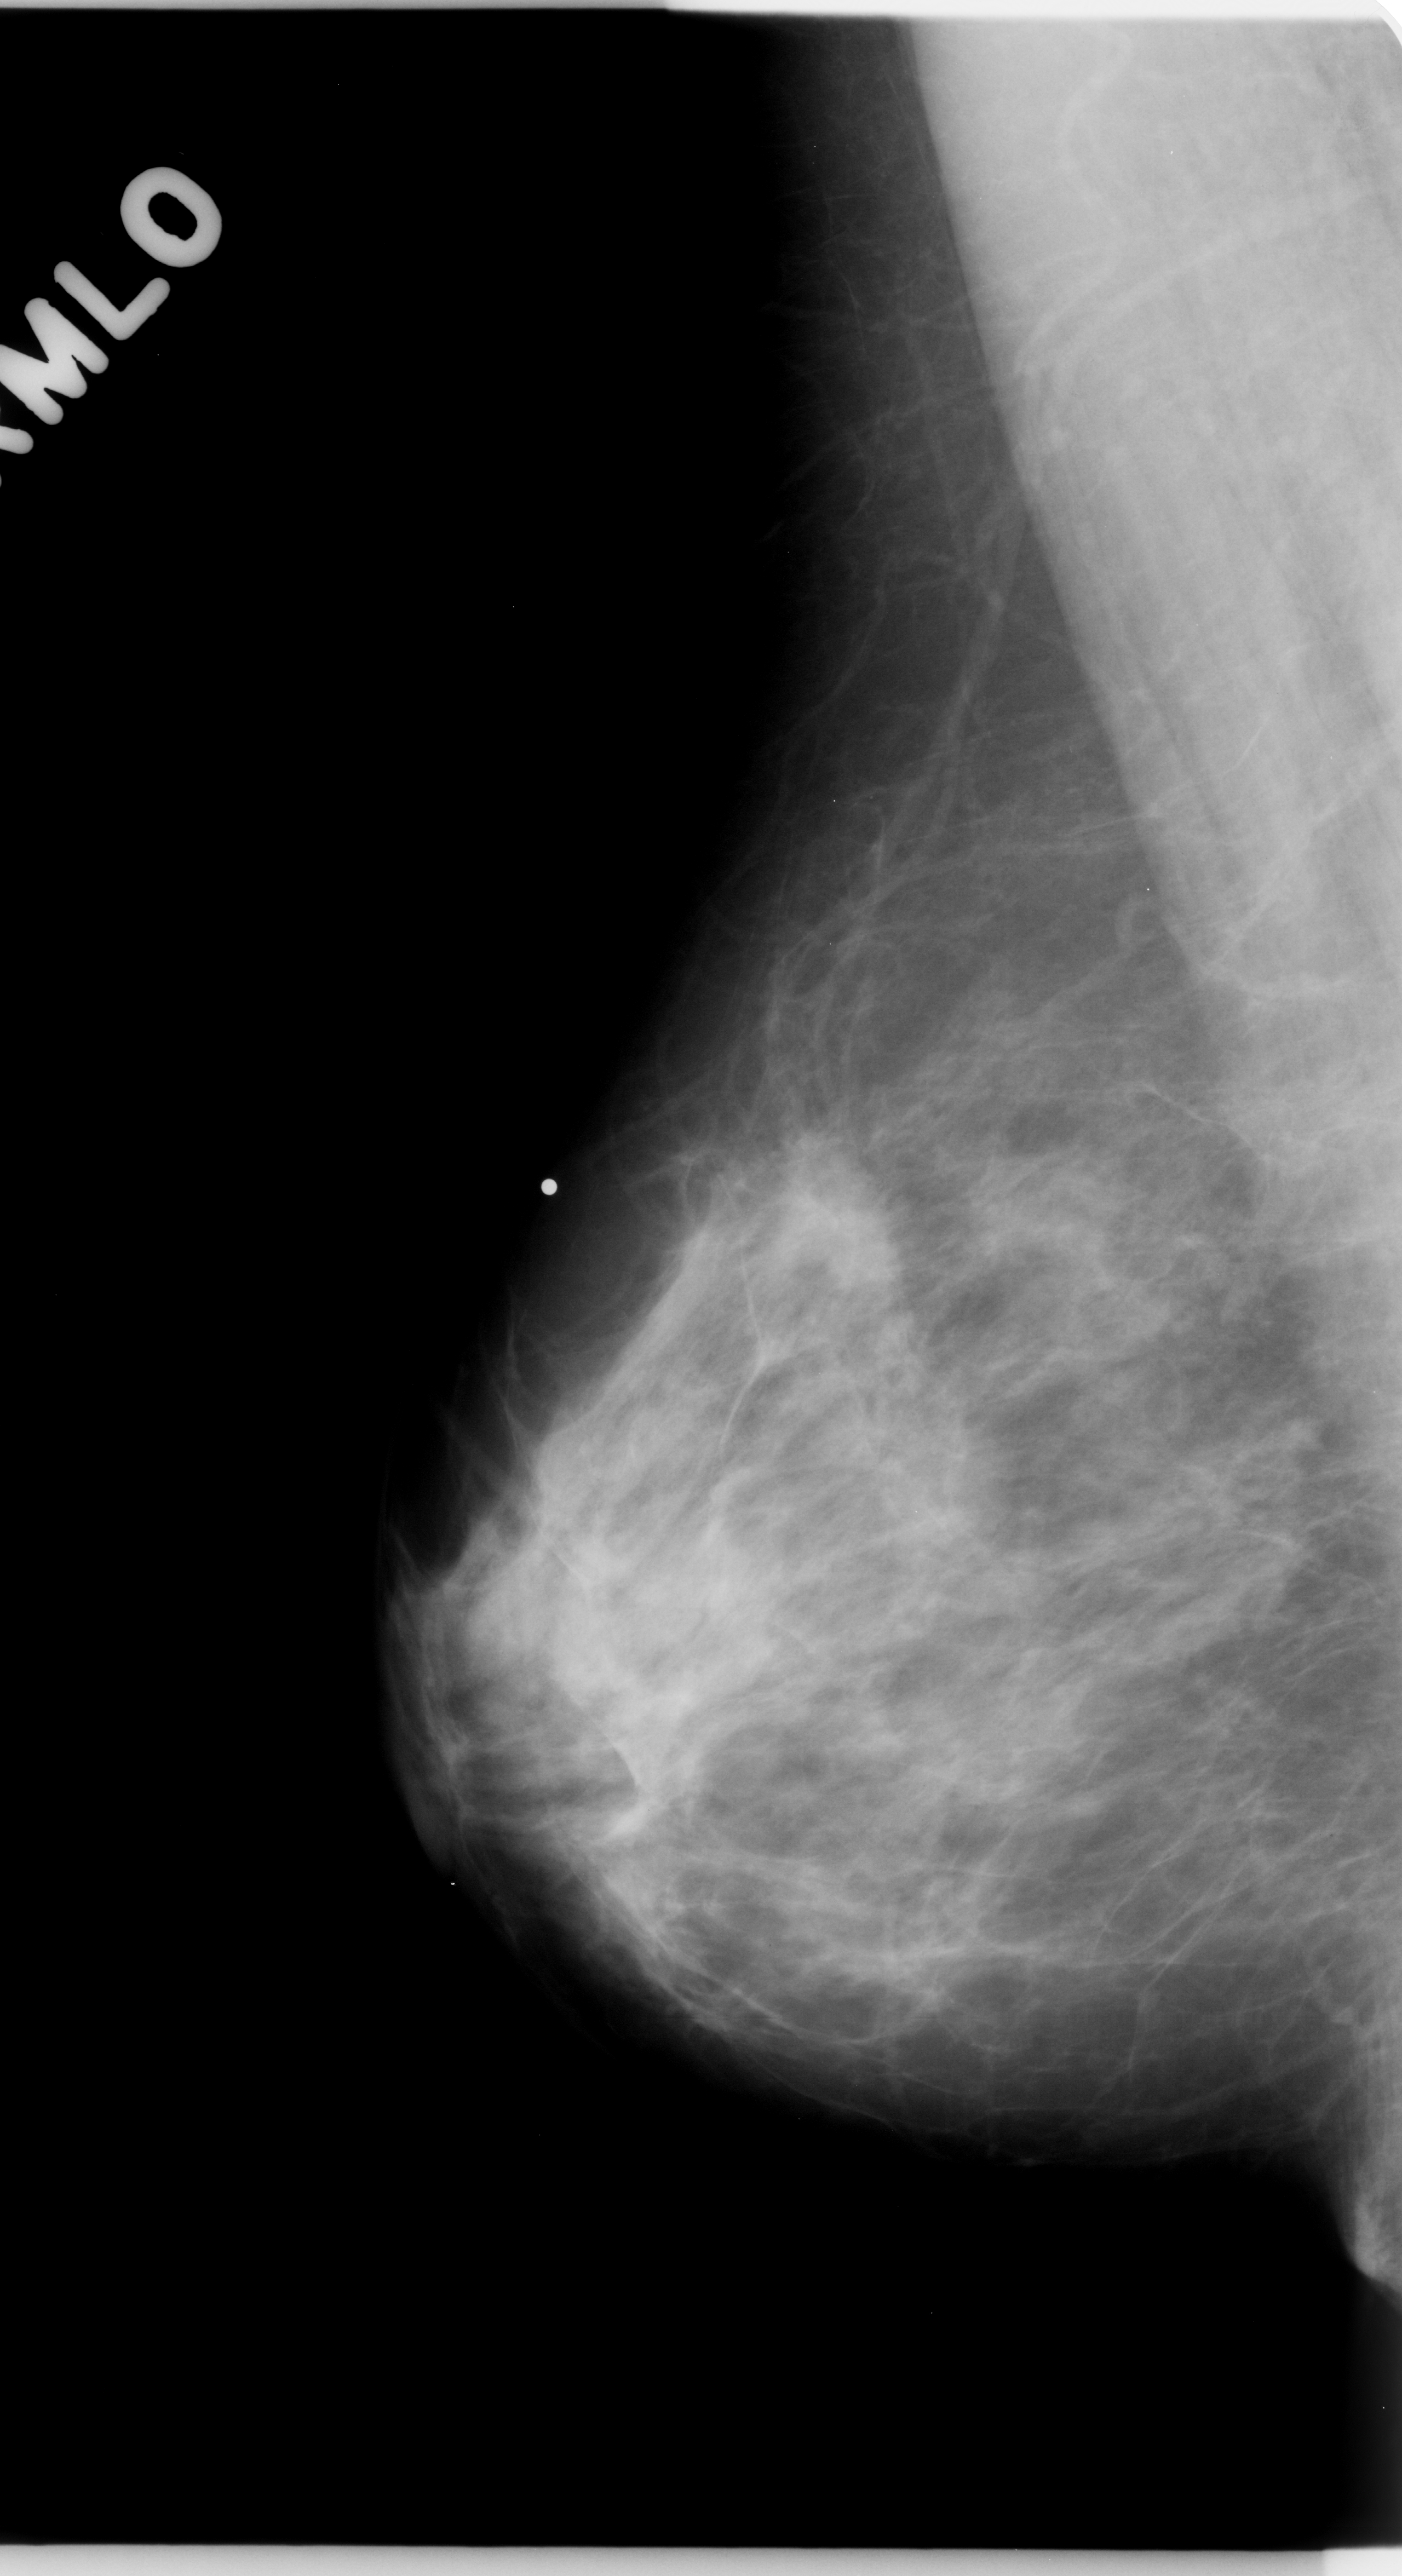
Digitized screen-film mammogram. Right breast. Mediolateral oblique (MLO) view. Breast composition: scattered fibroglandular densities (BI-RADS density category 2 of 4). 1402 × 2576 image matrix.
Expert-marked regions of interest on this film, with their recorded descriptors:
- mass, shape irregular, margins spiculated; BI-RADS assessment category 5; subtlety rating 5 on a 1 (subtle) to 5 (obvious) scale; pathology (as recorded): malignant: bounding box (x1, y1, x2, y2) in pixels: (746, 1118, 920, 1329)